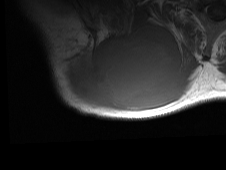
MRI of an extremity soft-tissue mass, one axial slice. Slice 50 of 81 in the series (ordered by position). MR volume resampled by the dataset authors to the PET/CT grid (not the native acquisition matrix). 3.27 mm slice thickness. 226 × 170 image matrix, field of view 221 × 166 mm. Male patient. From the clinical record (not read from this slice): histological type: pleiomorphic spindle cell undifferentiated; grade: high; site of the primary tumour: right parascapusular.
Outlined on this slice (expert contour drawn on MRI and transferred to this co-registered scan by the dataset authors):
- gross tumour volume including surrounding oedema: bounding box (x1, y1, x2, y2) in pixels: (60, 24, 200, 114)
- gross tumour volume (mass): (64, 26, 184, 110)